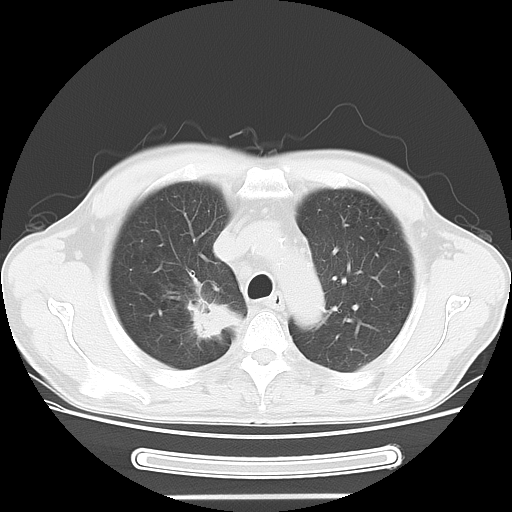
Chest CT, one axial slice. Slice 38 of 51 in the series (ordered by position). Reconstruction kernel LUNG. Lung window (W 1500 / L -600 HU). 5 mm slice thickness. 512 × 512 image matrix, field of view 350 × 350 mm. Patient: male, 57 years. From the clinical record (not read from this slice): clinical TNM (as recorded): T2 N3 M1b.
Outlined on this slice (bounding box drawn by a radiologist):
- lung tumour (recorded histology: adenocarcinoma): box from (x=190, y=297) to (x=234, y=342) px